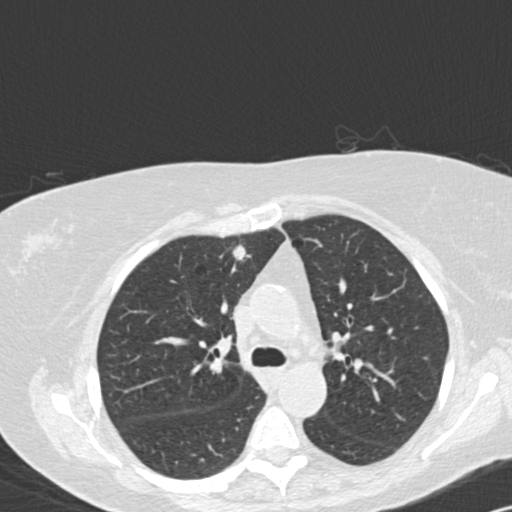
Low-dose screening chest CT, one axial slice. Slice 98 of 141 in the series (ordered by position). 120 kVp. Lung window (W 1500 / L -600 HU). 512 × 512 image matrix, field of view 328 × 328 mm.
Annotated regions visible in this slice (manually delineated by an expert):
- lesion 1 (tumor, upper lobe of right lung): bounding box <233,245,247,260> (left, top, right, bottom; pixels)